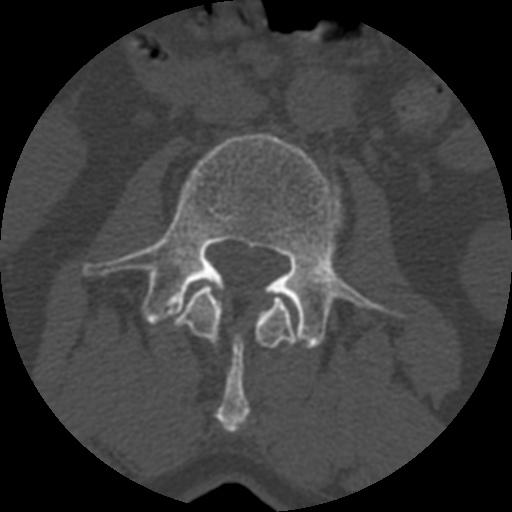
CT including the spine, one axial slice; slice 315 of 399 in the series (ordered by position); bone window (W 1800 / L 400 HU); 512 × 512 image matrix. Patient age 71 years. Case-level facts recorded for this patient, not image findings: primary cancer: prostate.
Outlined on this slice (semi-automatic segmentation, software-assisted and operator-edited):
- L2 vertebra: bounding box (x1, y1, x2, y2) in pixels: (174, 285, 294, 432)
- L3 vertebra: (82, 132, 406, 349)